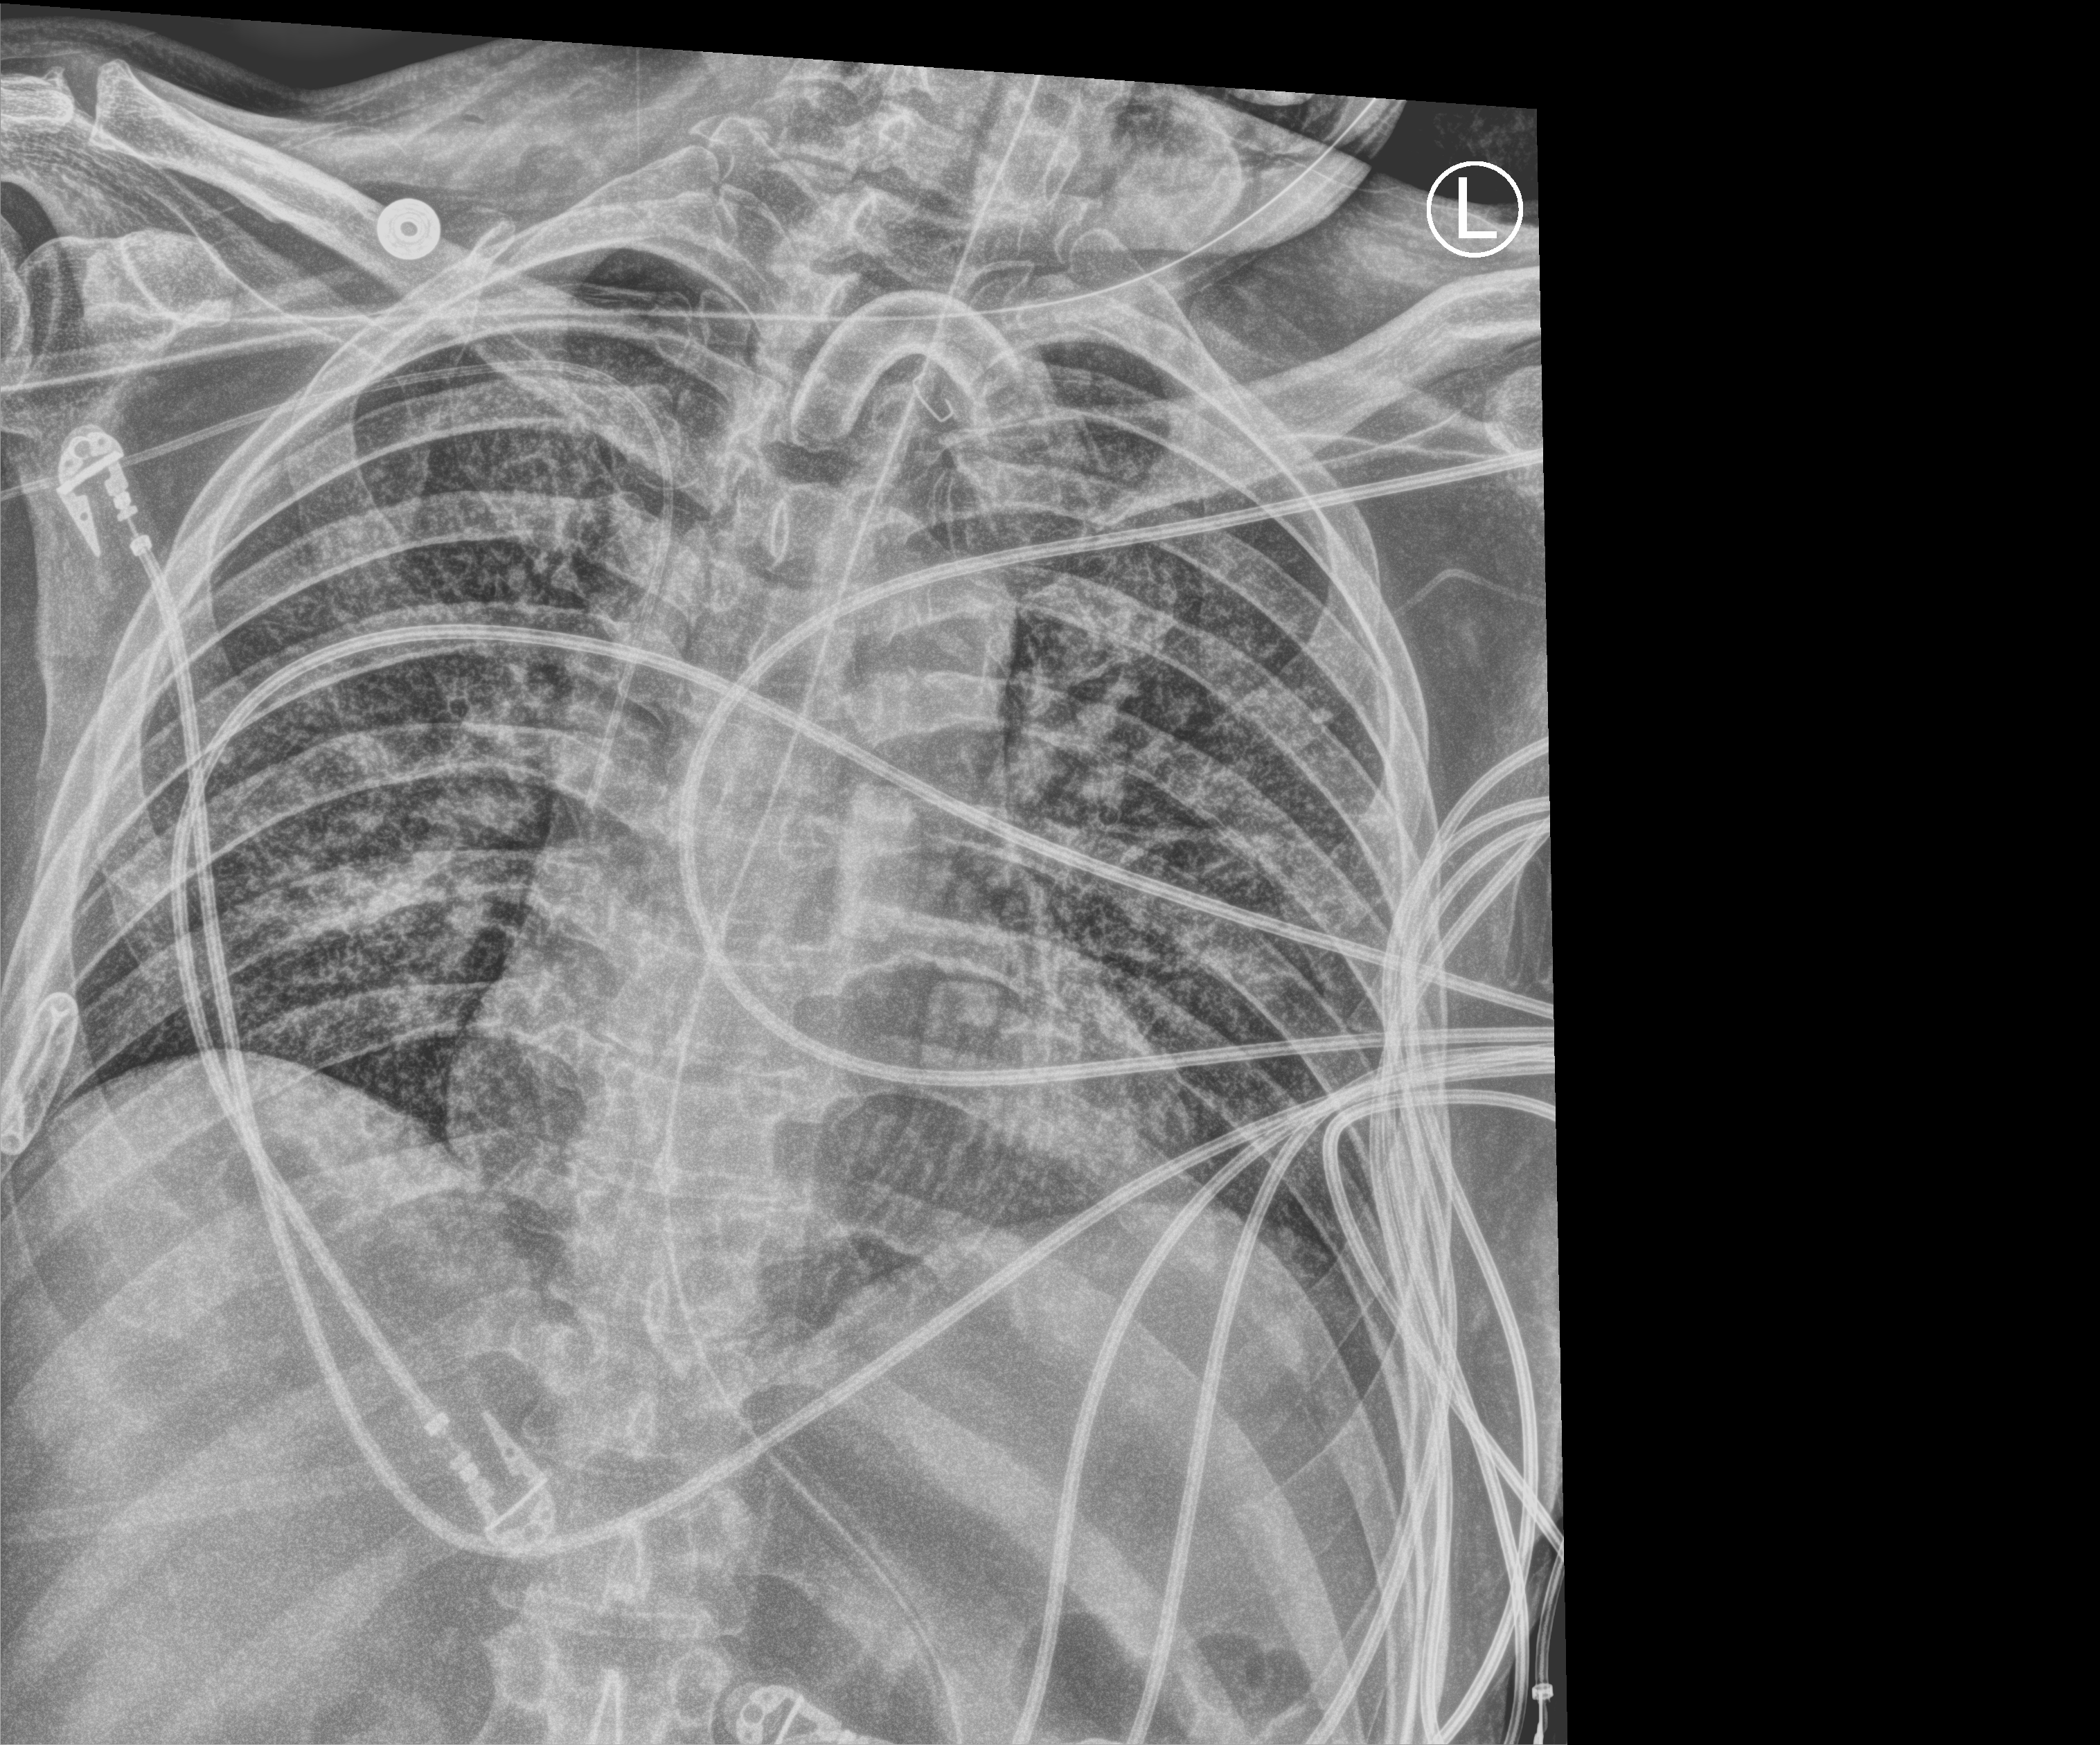
Chest X-ray (portable); anteroposterior (AP) projection. Patient hospitalised with COVID-19; male, aged 18–59 years.
From the hospital-stay record, not from the radiograph (when in the stay this image was taken is not recorded): COPD (admission record): no; chronic kidney disease (admission record): no.